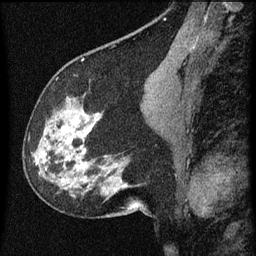
Breast MRI (dynamic contrast-enhanced), one sagittal slice. Position 31 of 60 along the scan axis. Dynamic contrast-enhanced series, image 2 of 3 at this slice position (ordered by acquisition). 1.5 T. TE 4.2 ms, TR 8 ms. 2 mm slice thickness. 256 × 256 image matrix, field of view 180 × 180 mm. Female patient, age 61 years.
Outlined on this slice (semi-automatically segmented with operator editing):
- analysis volume of interest (the breast-tissue region the enhancement analysis was run in; not a lesion): bounding box (x1, y1, x2, y2) in pixels: (27, 80, 139, 209)
- tumour enhancement mask (voxels above the 70 % enhancement threshold inside the analysis volume of interest): (36, 114, 97, 165)